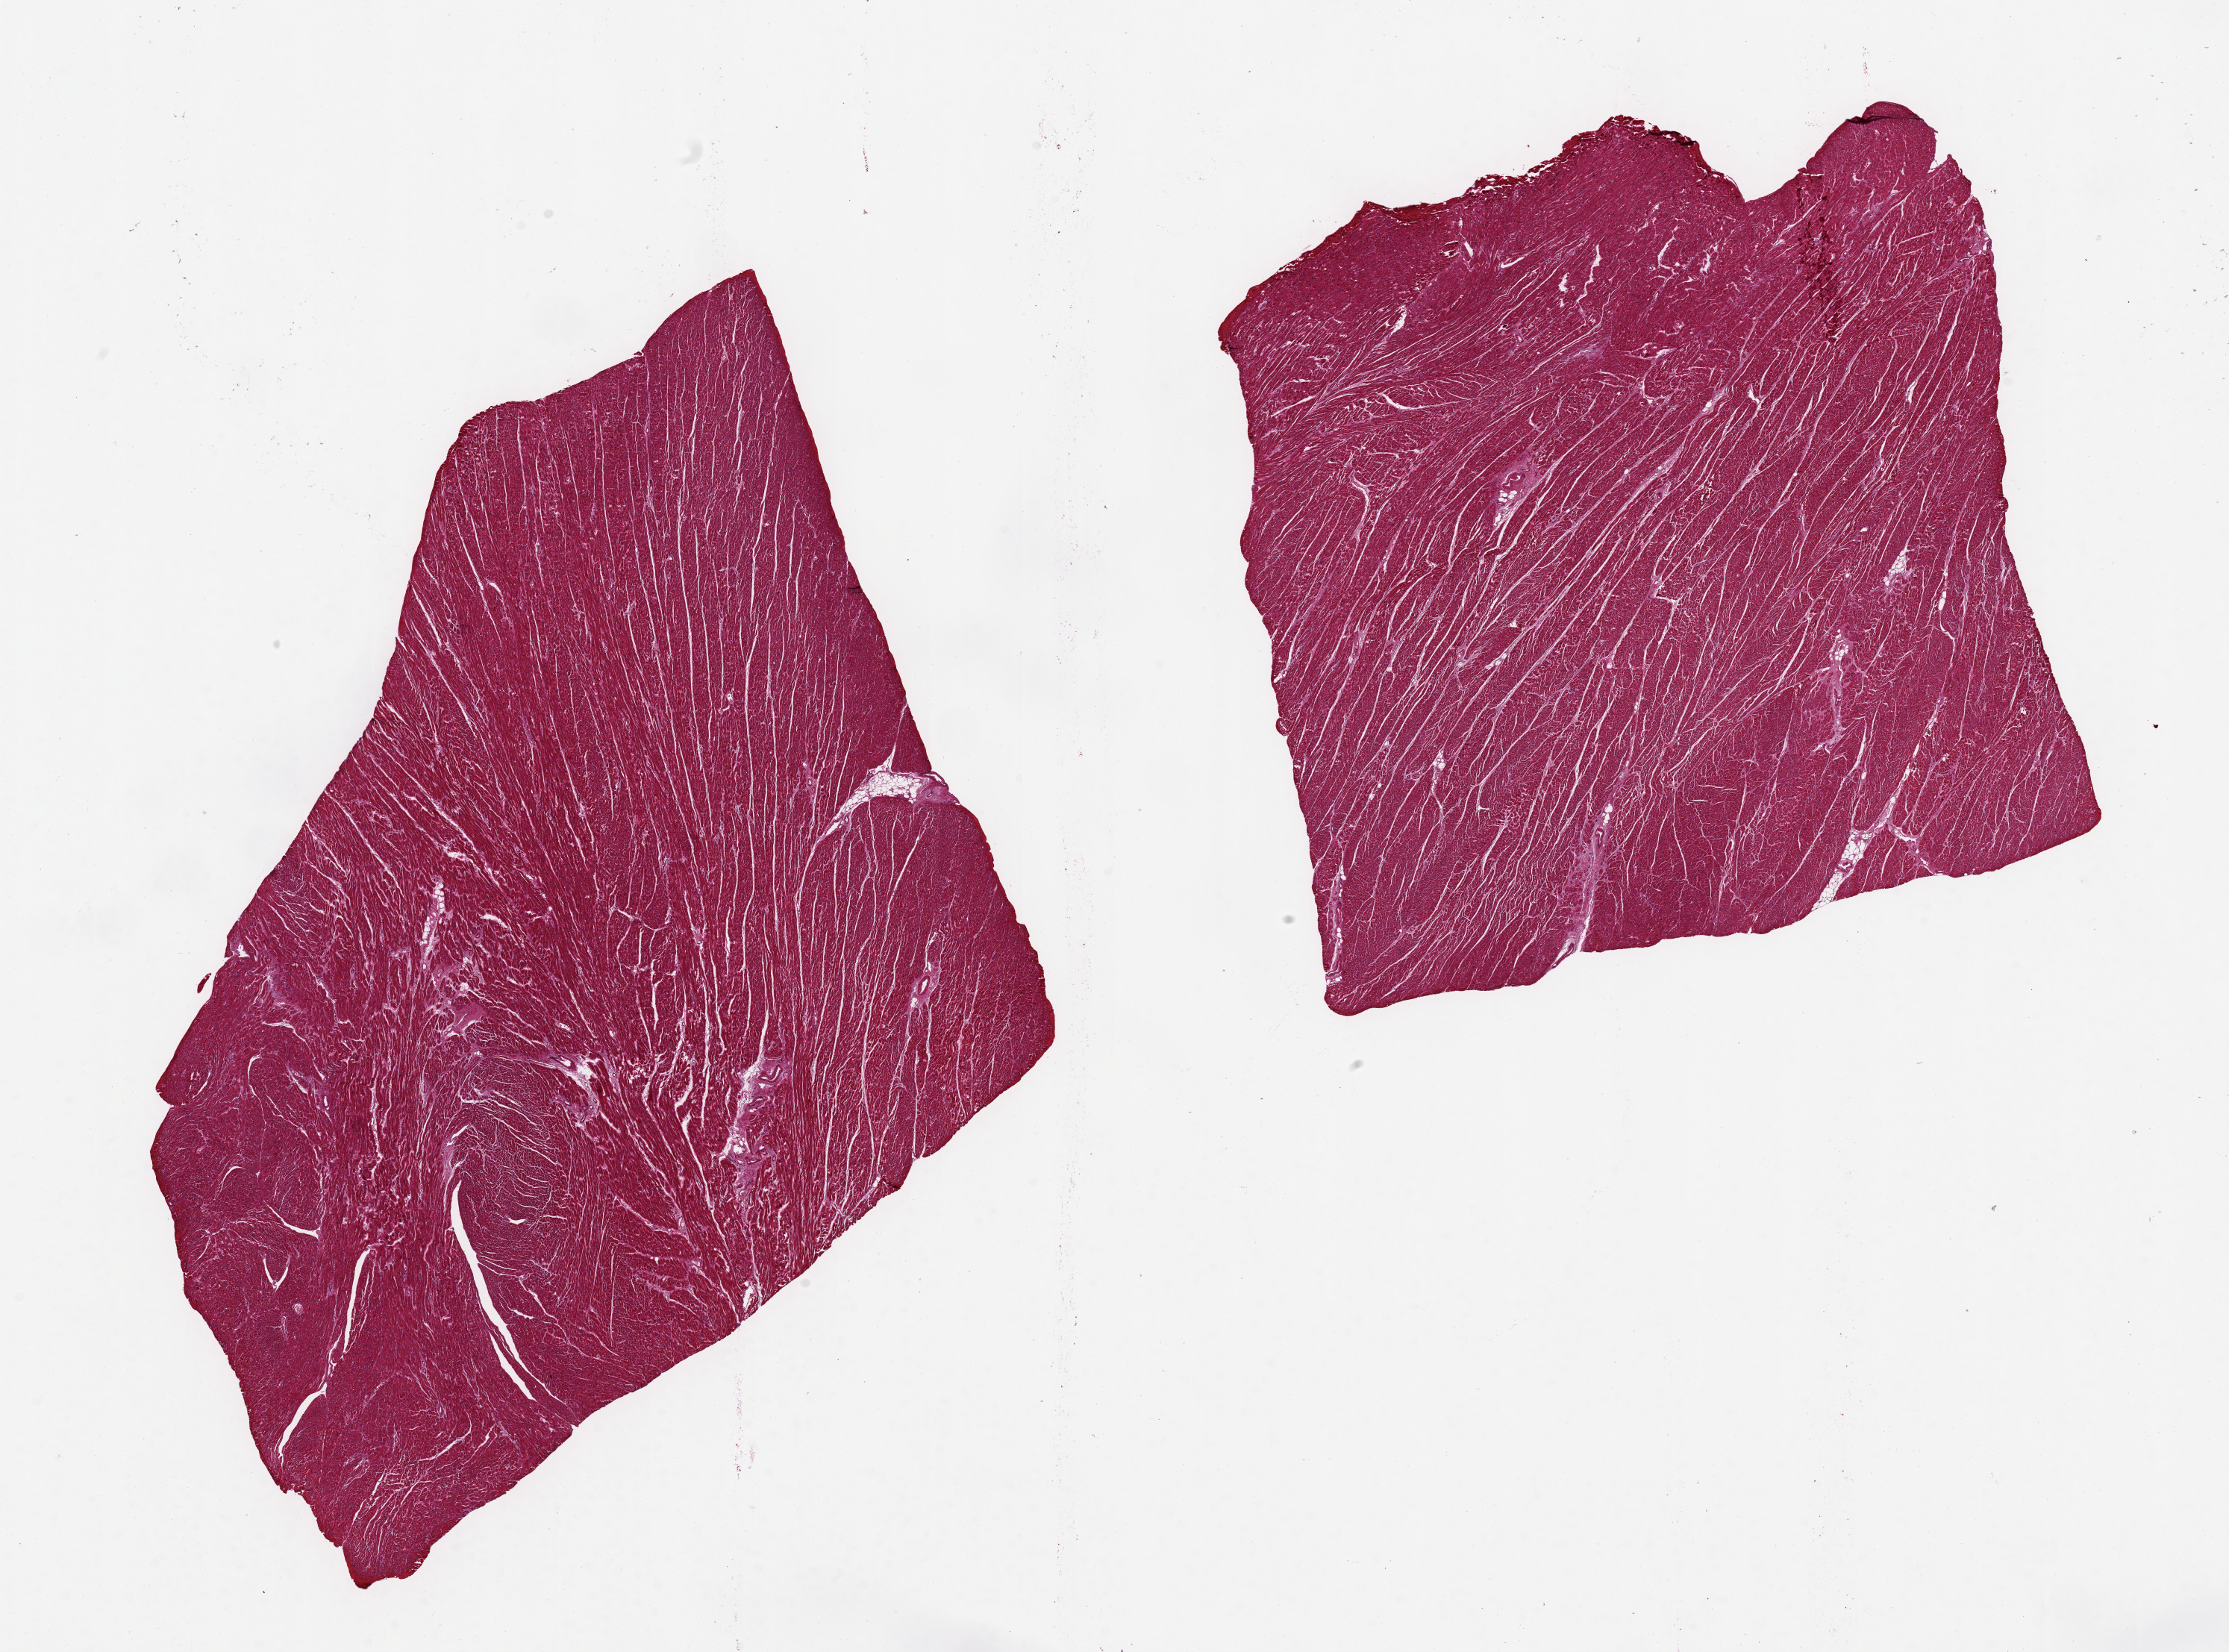
Digitized hematoxylin and eosin (H&E)-stained section, shown as a low-resolution overview of the whole scanned area (about 23.6 x 17.5 mm); PAXgene-fixed paraffin-embedded (PFPE) section; sampled site (target tissue): heart; donor tissue sample.
* review note (as recorded): 2 pieces 10x9 & 8x8 mm